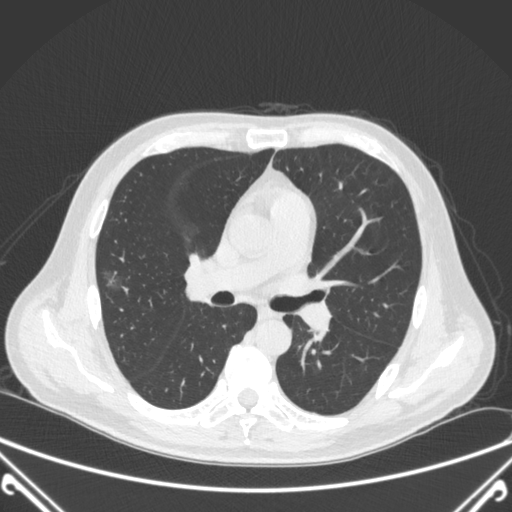
Chest CT, one axial slice; position 217 of 360 along the scan axis; lung window (W 1500 / L -600 HU); 1 mm slice thickness; 512 × 512 image matrix. Patient: male, 64 years. From the clinical record (not read from this slice): clinical TNM (as recorded): T1c N0 M0.
Outlined on this slice (rectangle marked by the reading radiologist):
- lung tumour (recorded histology: adenocarcinoma): box from (x=104, y=267) to (x=128, y=301) px